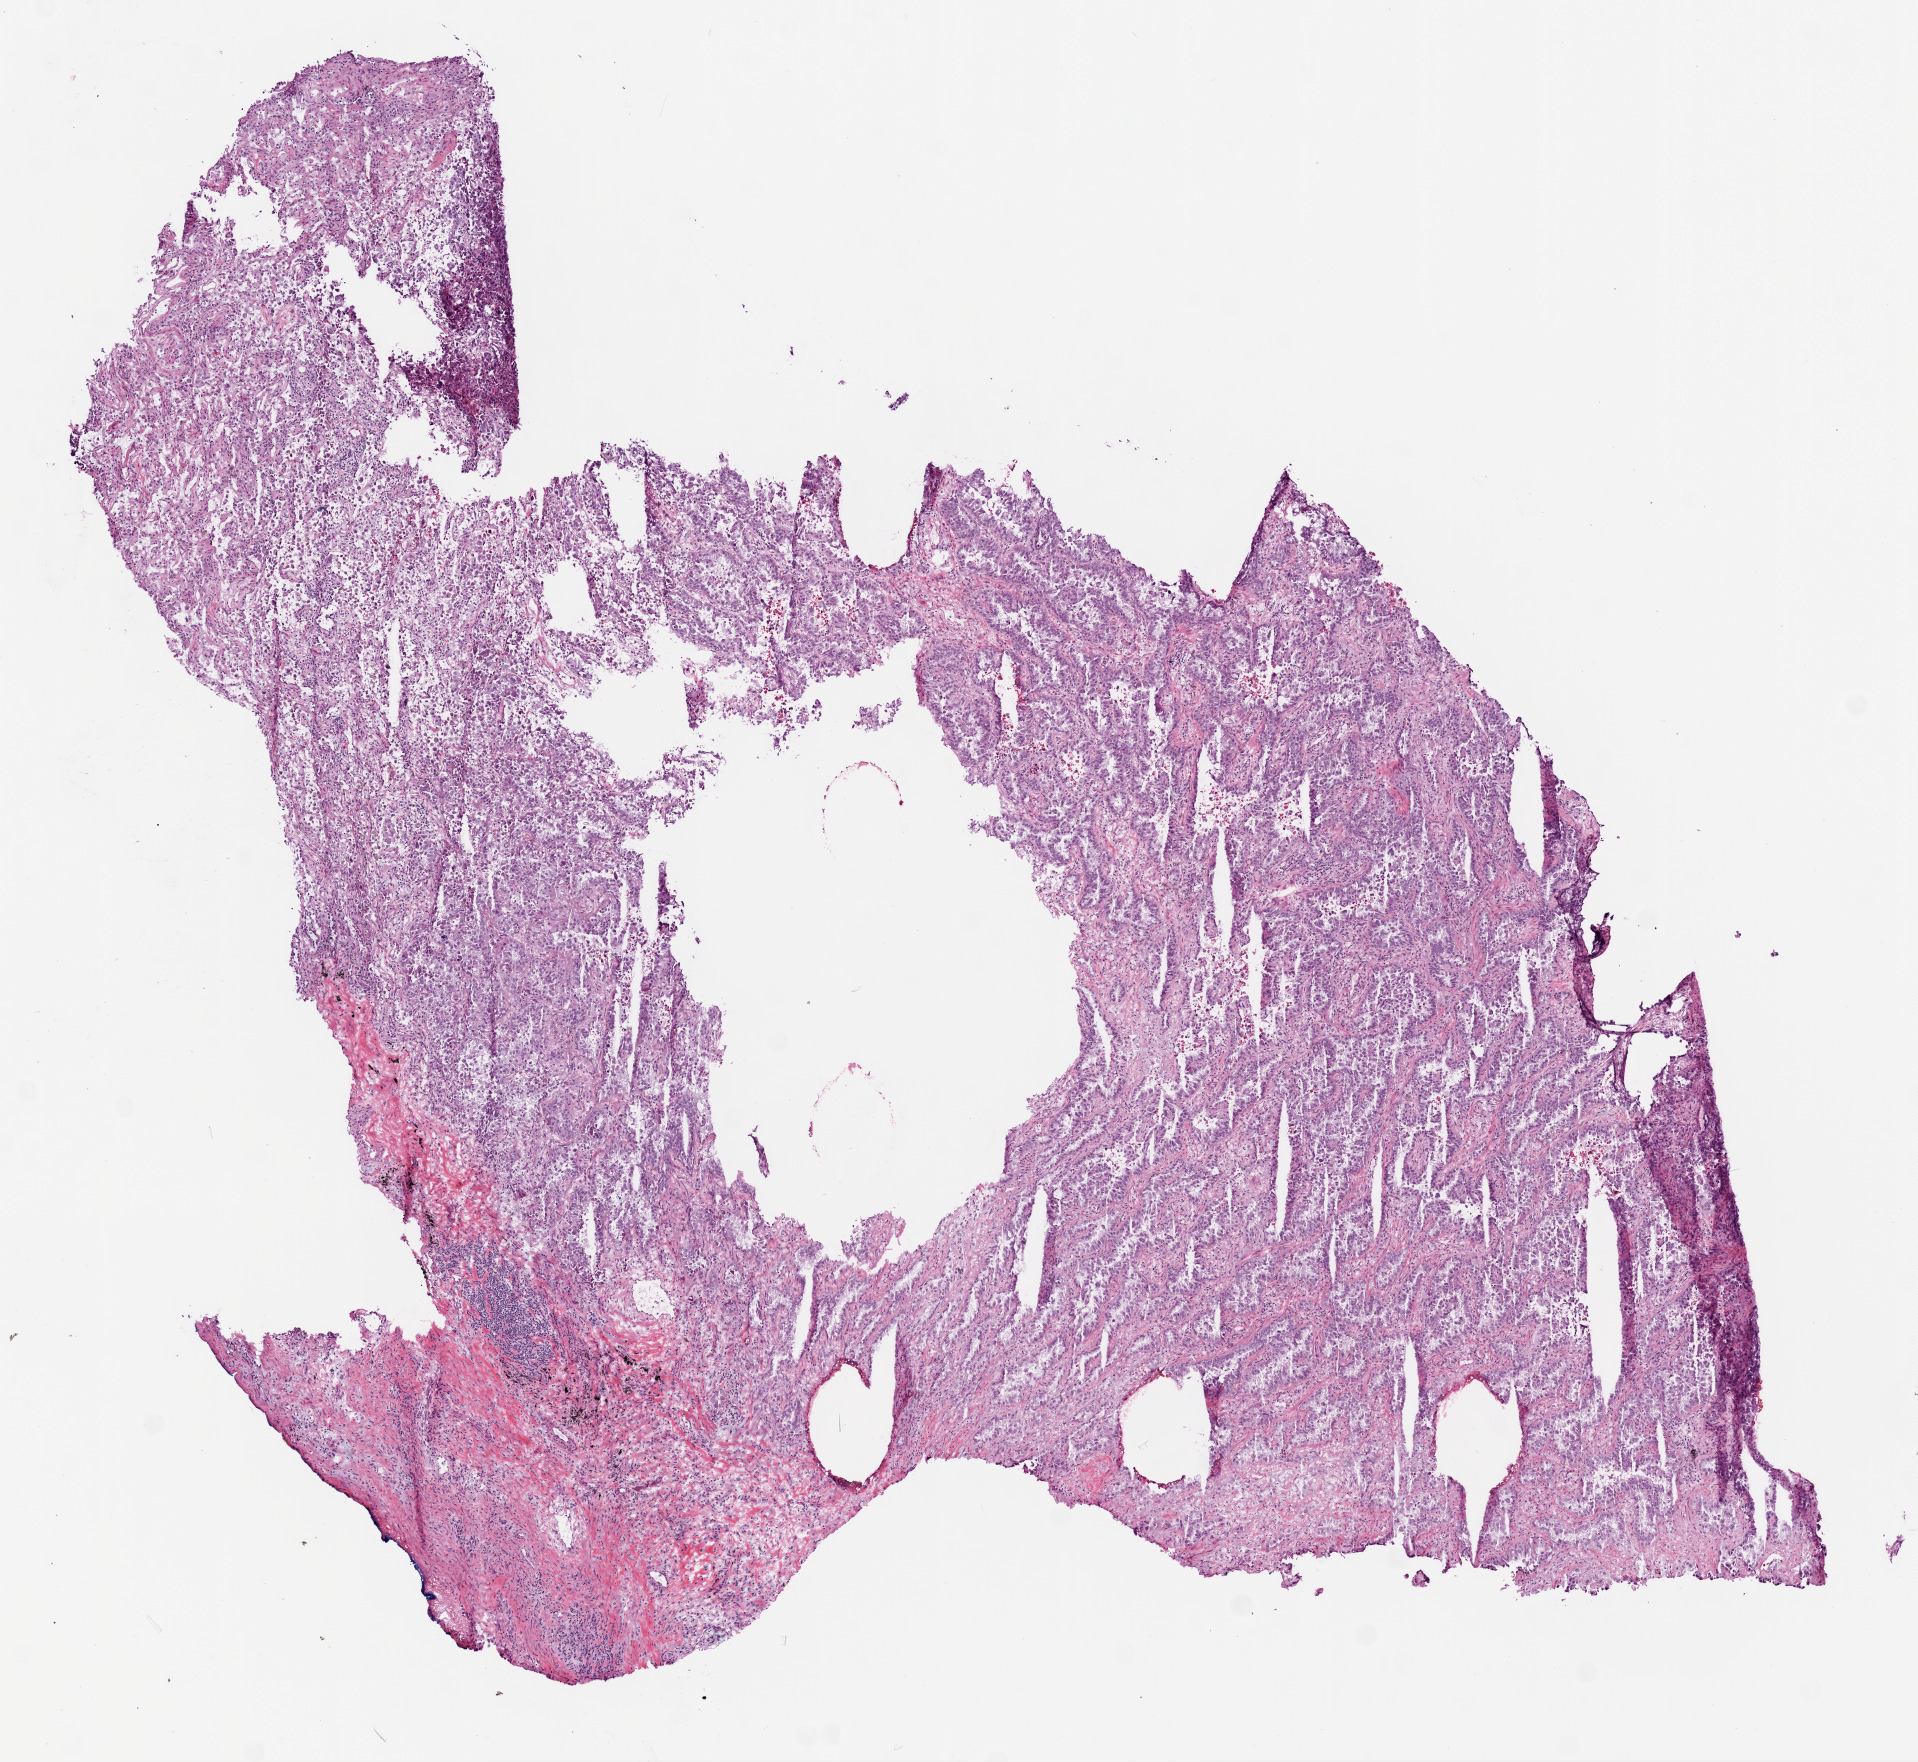
Digitized H&E tissue section (whole slide), whole scanned area (about 7.7 x 7.1 mm, slide scanned at 20x) shown as a low-resolution overview; frozen section from the top of the tissue portion; lung, primary tumour sample. Male patient; age at initial diagnosis 73 years. Slide review estimates, as recorded: tumour cells 70%, tumour nuclei 65%, normal cells 0%, stromal cells 25%, necrosis 5%.
TNM: T3 N0 M0. Histologic diagnosis: Adenocarcinoma with mixed subtypes (lower lobe, lung). AJCC pathologic stage: IIB (7th edition).